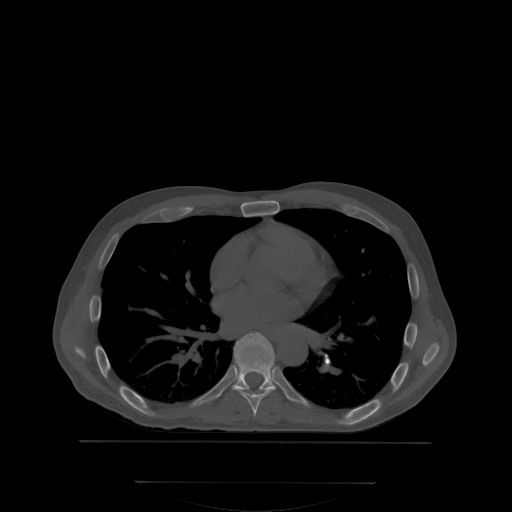
CT including the spine, one axial slice. Slice 221 of 350 in the series (ordered by position). Bone window (W 1800 / L 400 HU). 2.5 mm slice thickness. 512 × 512 image matrix. Patient: male, 58 years. From the clinical record (not read from this slice): primary cancer: prostate.
Structures marked on this image (semi-automatic segmentation, software-assisted and operator-edited):
- T7 vertebra: bounding box <232,372,282,415> (left, top, right, bottom; pixels)
- T8 vertebra: <208,333,275,395>